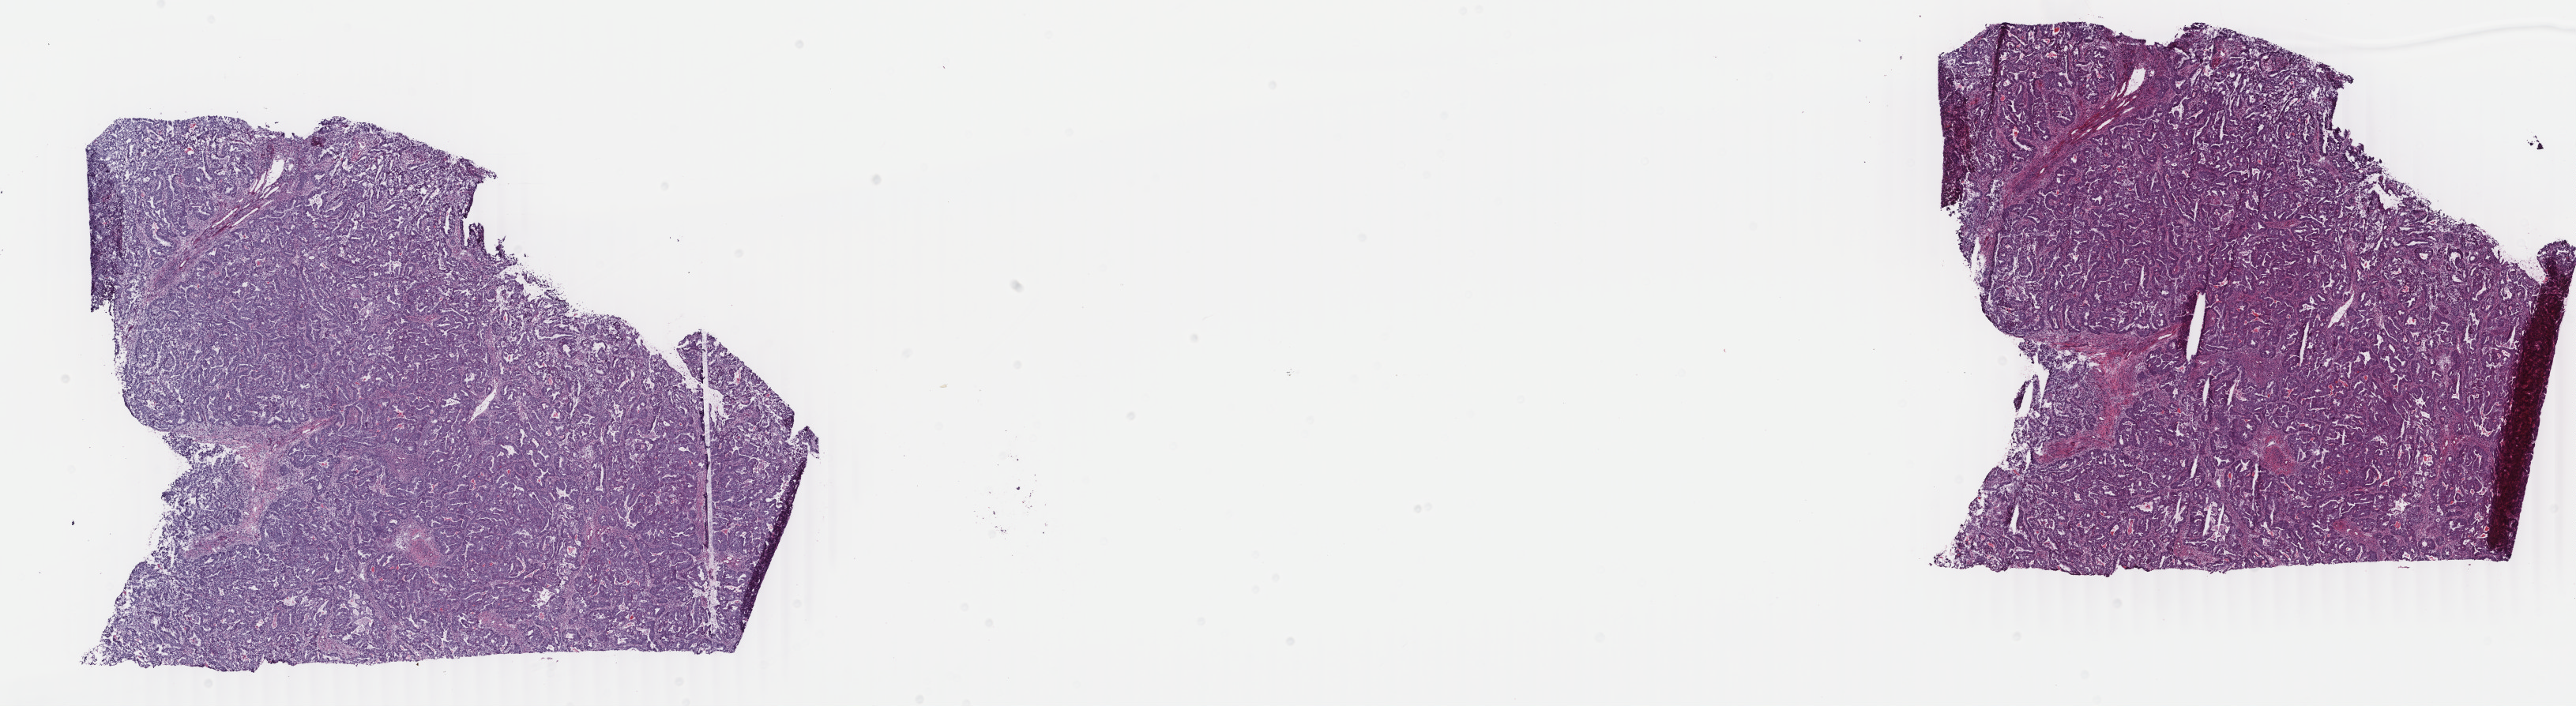
Whole-slide histology image, Hematoxylin and eosin (H&E) stained, low-resolution overview of the scanned area, about 25.9 x 7.1 mm. Frozen section from the bottom of the tissue portion. Sample: primary tumour, uterus. Female, age 49 years at initial diagnosis. Histologic grade: G2 (moderately differentiated). Pathologist review of this section (percent, as recorded): tumour cells 100%, tumour nuclei 75%, normal cells 0%, stromal cells 0%, necrosis 0%. Infiltration values recorded for this section: lymphocyte infiltration 0%, monocyte infiltration 0%, neutrophil infiltration 0%.
• lymph nodes positive (case pathology): 0 of 45 examined
• FIGO stage: IB
• diagnosis: Endometrioid adenocarcinoma, NOS (endometrium)